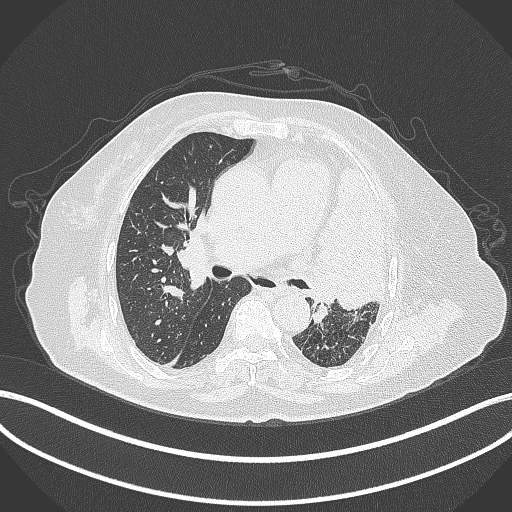
Chest CT, one axial slice; slice 222 of 399 in the series (ordered by position); reconstruction kernel B70f; 120 kVp; lung window (W 1500 / L -600 HU); 1 mm slice thickness; 512 × 512 image matrix. Patient: female, 75 years. From the clinical record (not read from this slice): clinical TNM (as recorded): T3 N3 M1.
Structures marked on this image (rectangle marked by the reading radiologist):
- lung tumour (recorded histology: adenocarcinoma): bounding box <305,151,394,311> (left, top, right, bottom; pixels)